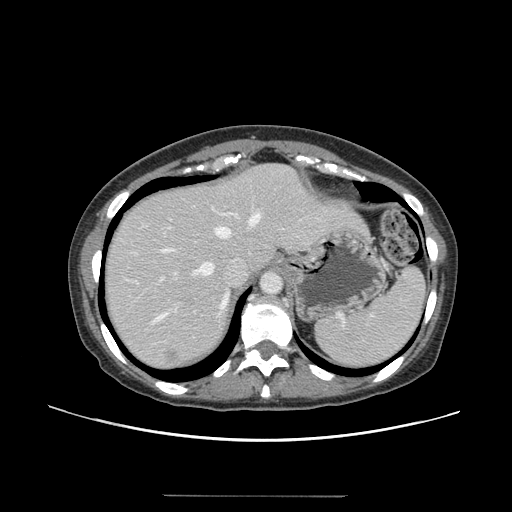
Contrast-enhanced abdominal CT, one axial slice. Slice 115 of 144 in the series (ordered by position). 120 kVp. Soft-tissue window (W 400 / L 40 HU). 512 × 512 image matrix, field of view 380 × 380 mm. Female patient, age 53 years. Case-level facts recorded for this patient, not image findings: diagnosis: colorectal cancer liver metastases, imaged before liver resection; multiple liver metastases: yes; largest metastasis: 1.1 cm; disease in both lobes: no.
Outlined on this slice (expert manual segmentation):
- hepatic veins: bounding box (x1, y1, x2, y2) in pixels: (154, 213, 262, 321)
- liver: (105, 165, 363, 369)
- planned liver remnant (the part of the liver to remain after resection): (104, 165, 290, 300)
- portal vein (with intrahepatic branches): (159, 219, 177, 282)
- liver metastasis: (181, 294, 194, 304)
- liver metastasis: (165, 350, 179, 363)